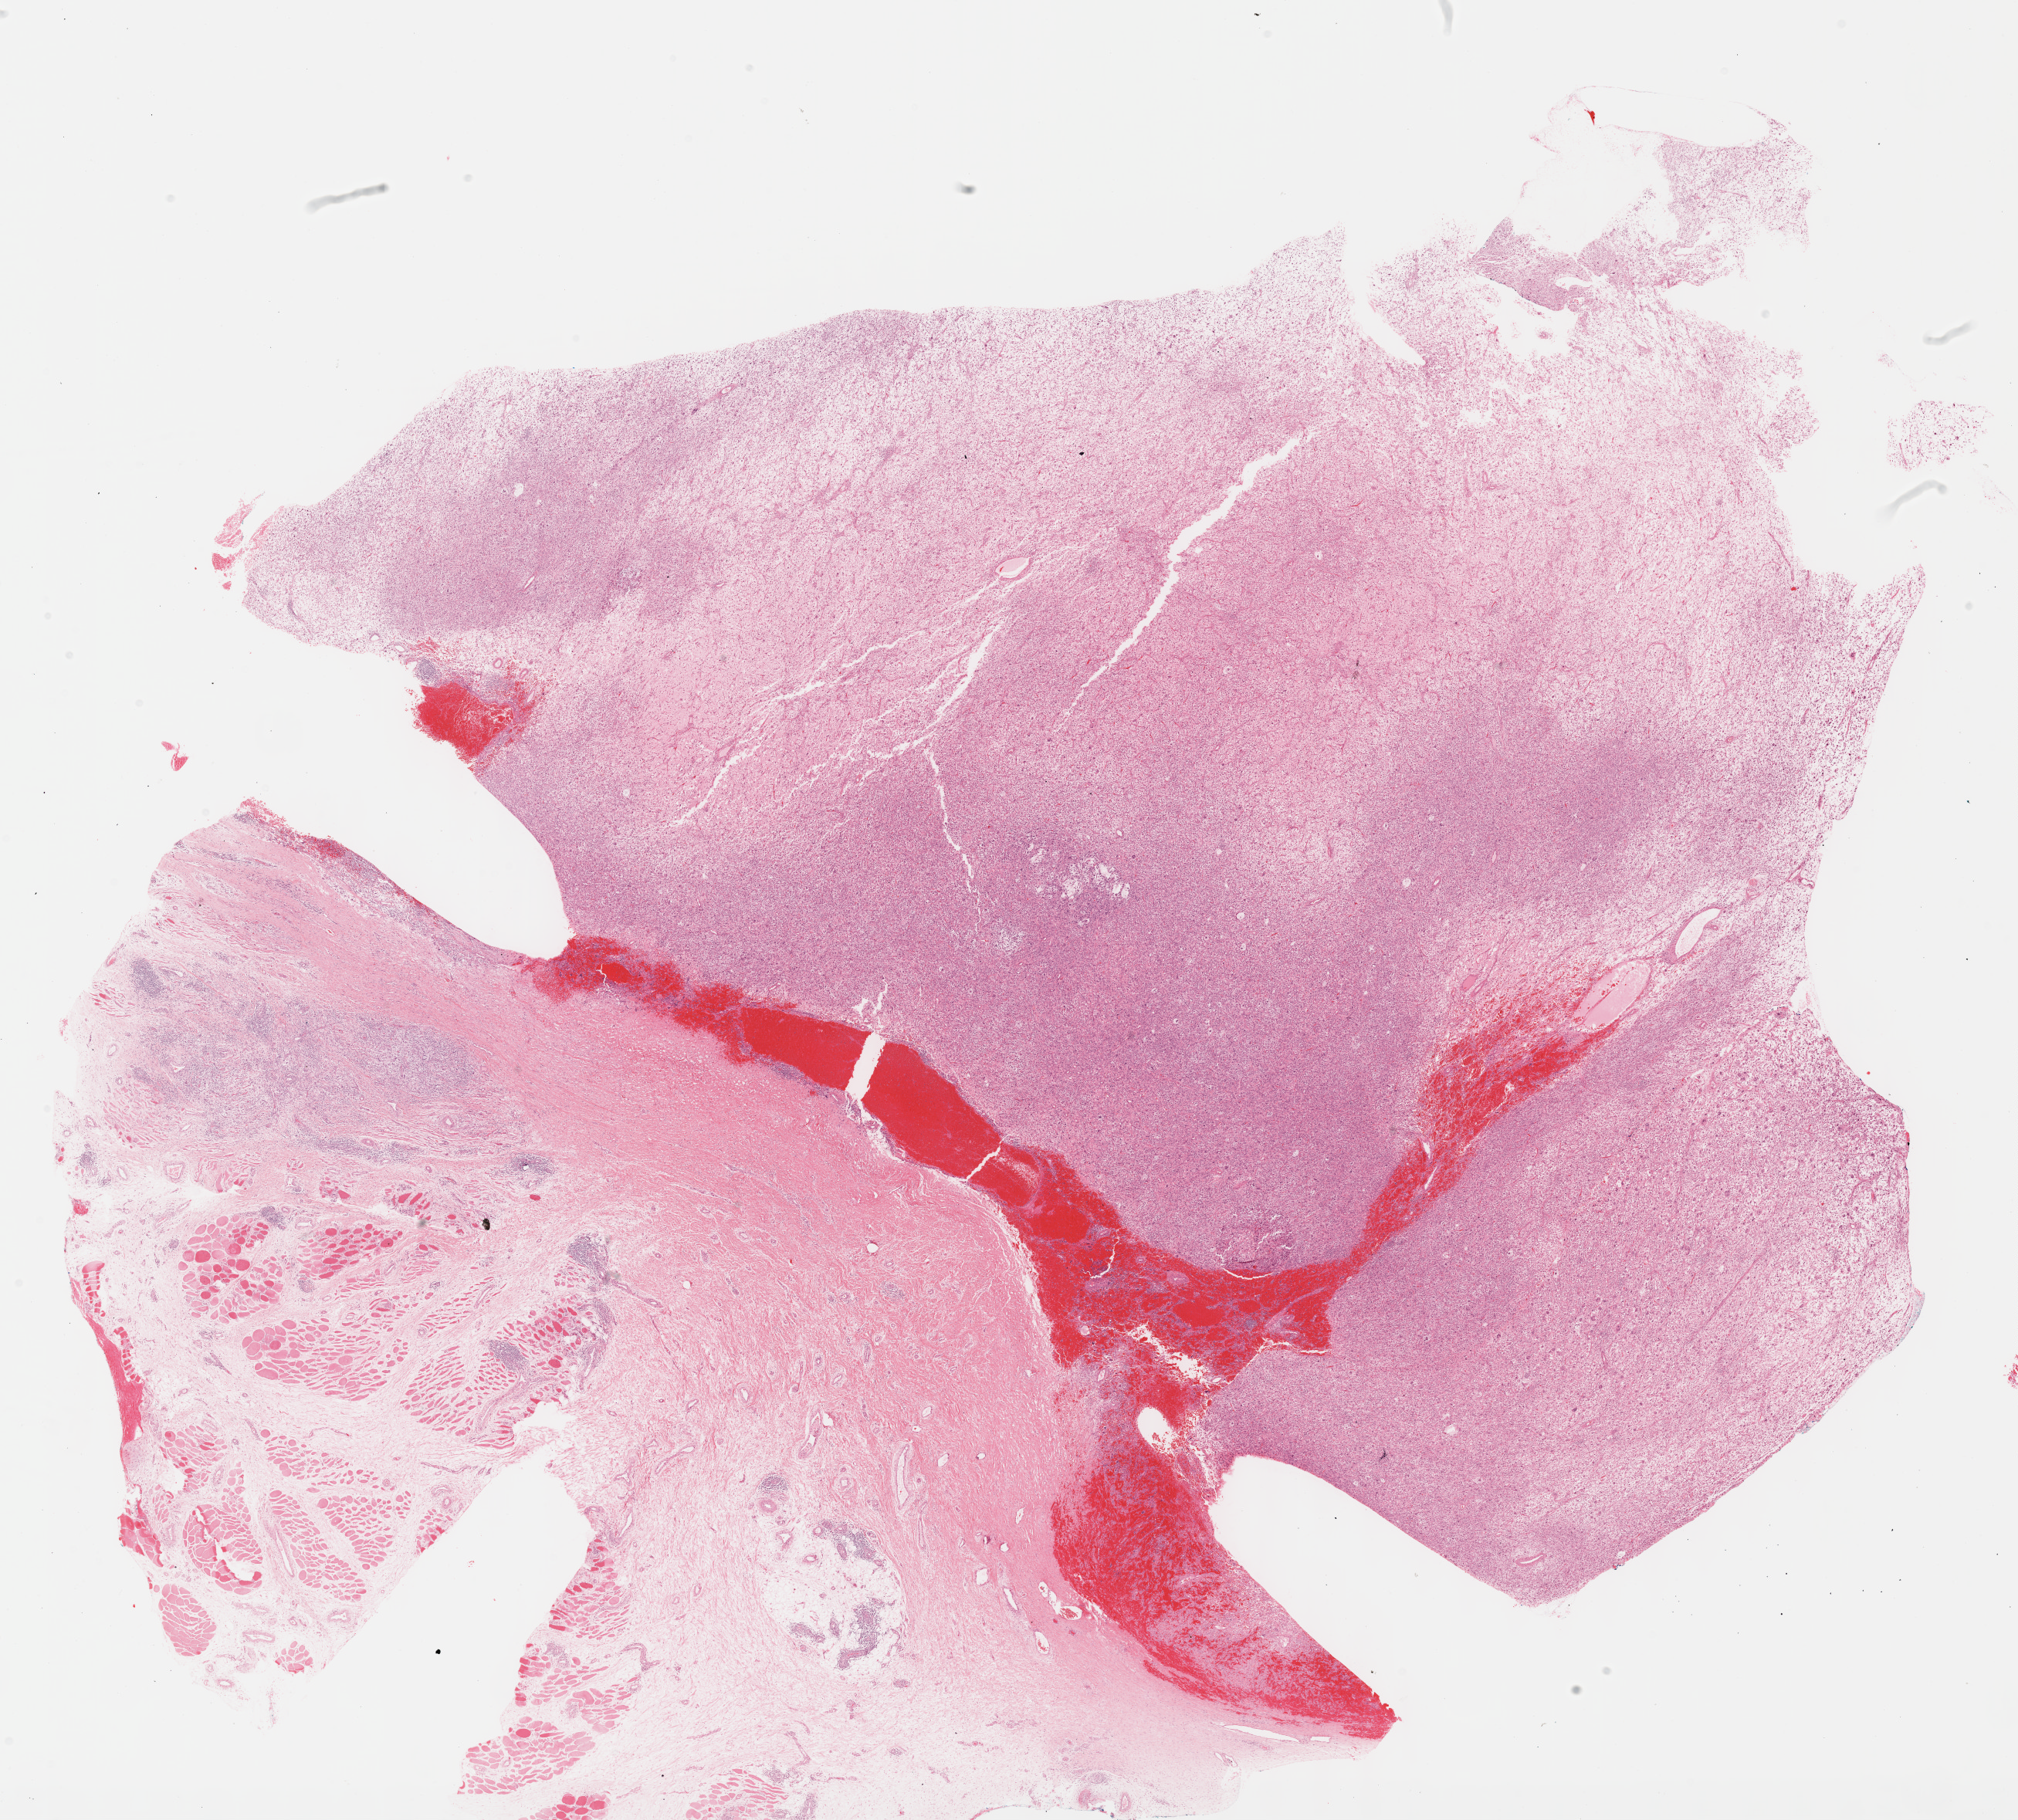
Whole-slide histology image, H&E, whole scanned area (about 21.1 x 19.1 mm, from a 40x scan) shown as a low-resolution overview; FFPE section; sample: primary tumour, connective, subcutaneous and other soft tissues. Female patient; age at initial diagnosis 63 years.
Histologic diagnosis: Malignant fibrous histiocytoma.